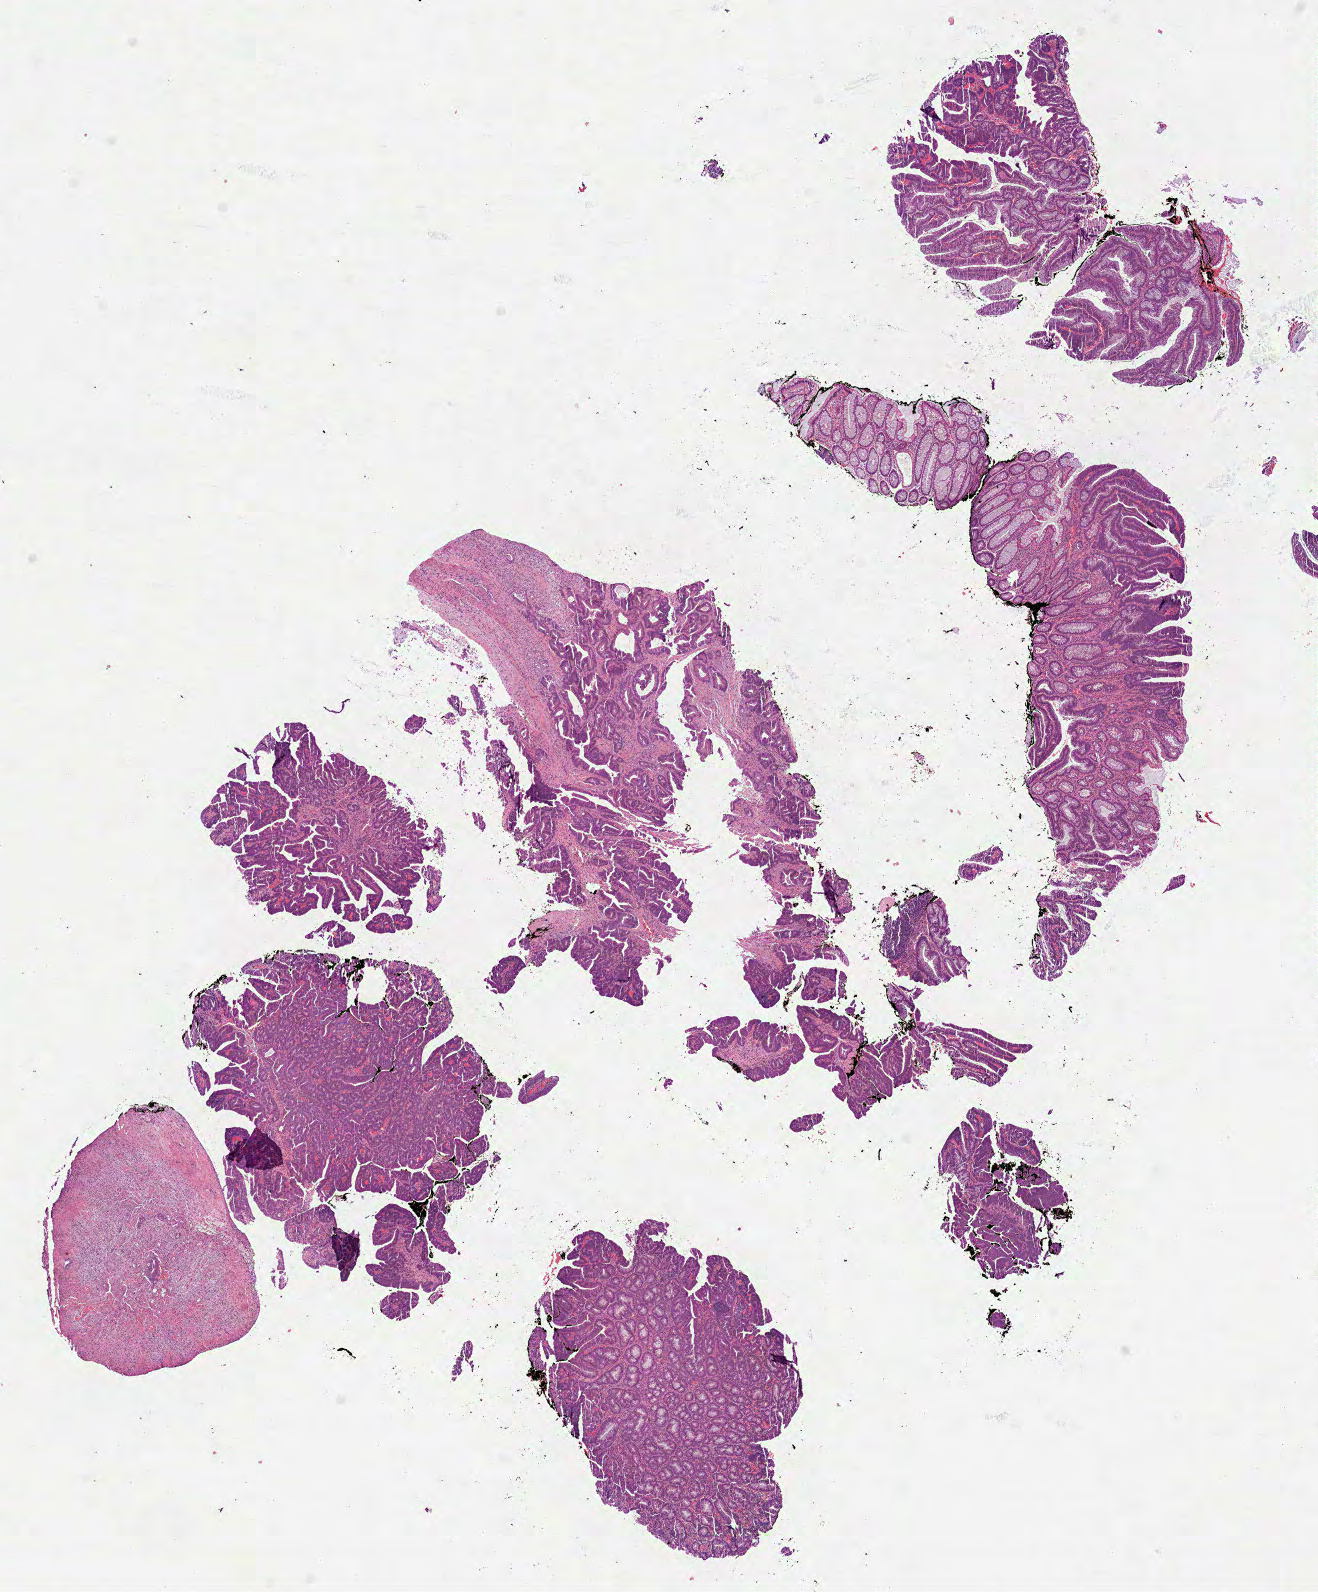
Digitized H&E-stained tissue section (whole slide), shown as a low-resolution overview of the whole scanned area (about 10.6 x 12.8 mm, acquisition: 40x scan). Formalin-fixed paraffin-embedded (FFPE) diagnostic section. Rectum, primary tumour sample. Patient: male, age at initial diagnosis 46 years.
Diagnosis: Mucinous adenocarcinoma (rectosigmoid junction). TNM: T3 N1b M0. AJCC pathologic stage: IIIB. Lymph nodes positive (case pathology): 3 of 18 examined.